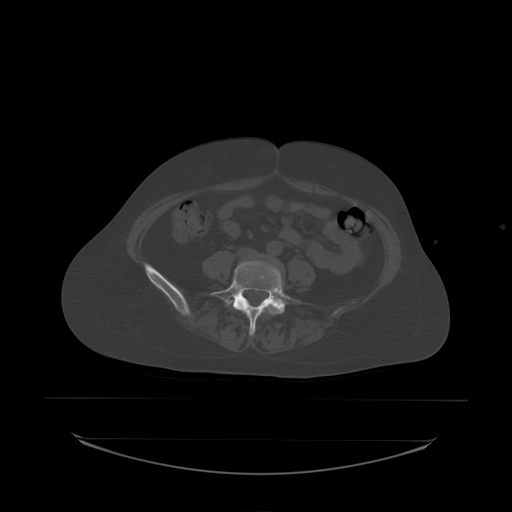
CT including the spine, one axial slice. Position 41 of 242 along the scan axis. Bone window (W 1800 / L 400 HU). 2.5 mm slice thickness. 512 × 512 image matrix. Female patient, age 53 years. From the clinical record (not read from this slice): primary cancer: lung; vertebrae with lytic lesions (as recorded): T7, L1.
Annotated regions visible in this slice (semi-automatic segmentation, software-assisted and operator-edited):
- L5 vertebra: bounding box [x1, y1, x2, y2] px = [214, 261, 302, 337]